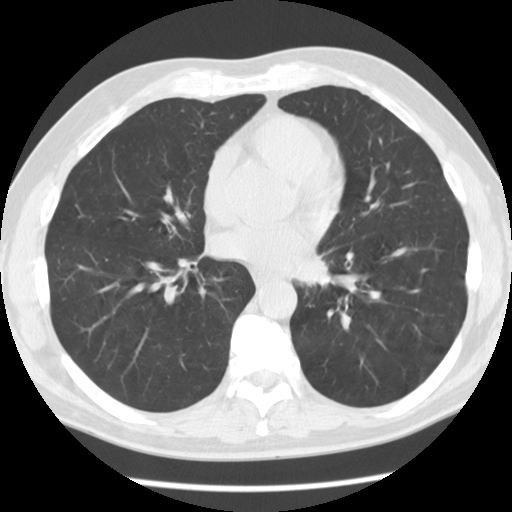
Axial slice from a low-dose chest CT screening exam; baseline annual screen; lung window (W 1500 / L -600 HU); 2.5 mm slice thickness; 120 kVp; slice 65 of 112 in the series; 512 × 512 image matrix. Male participant, aged 55 years at enrolment. Former smoker at enrolment.
Lesion marked by an expert reader, bounding box (x1, y1, x2, y2) in pixels: (283, 235, 347, 298). Screening reader's record for this exam: no non-calcified nodule ≥4 mm recorded. Lung cancer was diagnosed 223 days after this screen: squamous cell carcinoma, NOS, left lower lobe, moderately differentiated (G2), stage IV (AJCC 6th edition), 51 mm at pathology.